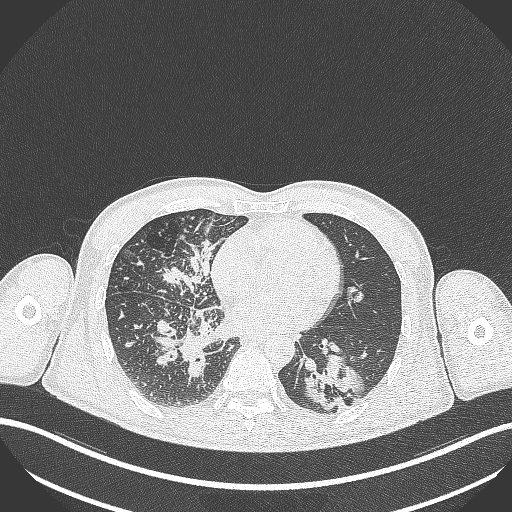
Chest CT, one axial slice; slice 128 of 348 in the series (ordered by position); 120 kVp; lung window (W 1500 / L -600 HU); 1 mm slice thickness; 512 × 512 image matrix, field of view 400 × 400 mm. Male patient, age 49 years. Case-level facts recorded for this patient, not image findings: clinical TNM (as recorded): T2b N1 M0.
Outlined on this slice (bounding box drawn by a radiologist):
- lung tumour (recorded histology: adenocarcinoma): bounding box <304,357,365,411> (left, top, right, bottom; pixels)